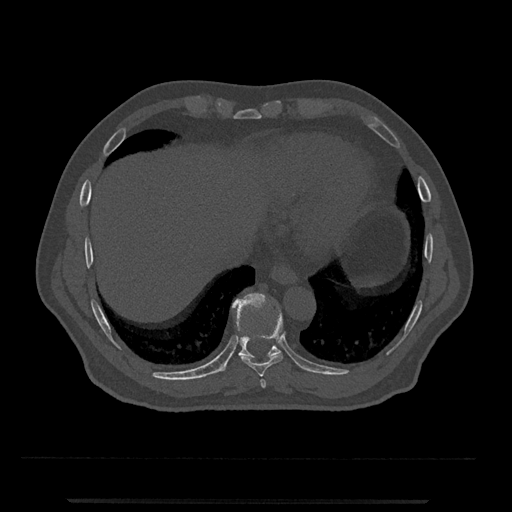
CT including the spine, one axial slice. Bone window (W 1800 / L 400 HU). 0.5 mm slice thickness. 512 × 512 image matrix, field of view 419 × 419 mm. Patient: male, 63 years. From the clinical record (not read from this slice): primary cancer: prostate.
Structures marked on this image (semi-automatically segmented with operator editing):
- T10 vertebra: bounding box (x1, y1, x2, y2) in pixels: (220, 293, 281, 372)
- T8 vertebra: (260, 379, 266, 388)
- T9 vertebra: (241, 307, 283, 377)